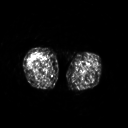
FDG PET of an extremity soft-tissue mass (from a PET/CT study), one axial slice; slice 211 of 311 in the series (ordered by position); 128 × 128 image matrix. Patient: female, 57 years. From the clinical record (not read from this slice): histological type: pleiomorphic undifferentiated sarcoma; grade: high; site of the primary tumour: right quadricep.
Structures marked on this image (expert contour drawn on MRI and transferred to this co-registered scan by the dataset authors):
- tumour plus oedema (research contour): bounding box <28,52,41,66> (left, top, right, bottom; pixels)